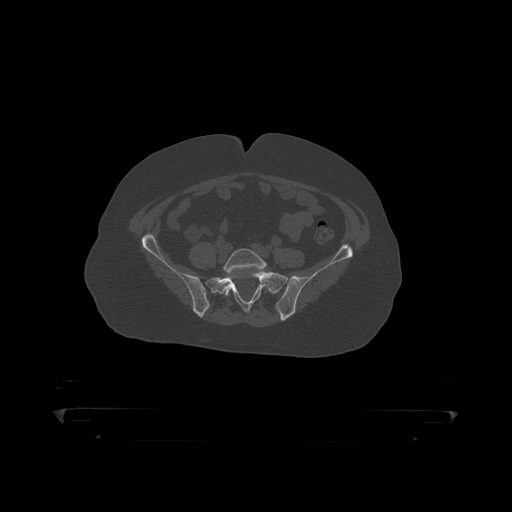
CT including the spine, one axial slice; slice 27 of 390 in the series (ordered by position); reconstruction kernel STANDARD; bone window (W 1800 / L 400 HU); 1.25 mm slice thickness; 512 × 512 image matrix, field of view 650 × 650 mm. Male patient, age 60 years. Case-level facts recorded for this patient, not image findings: primary cancer: prostate.
Annotated regions visible in this slice (semi-automatic segmentation, software-assisted and operator-edited):
- L5 vertebra: bounding box <224,249,269,297> (left, top, right, bottom; pixels)